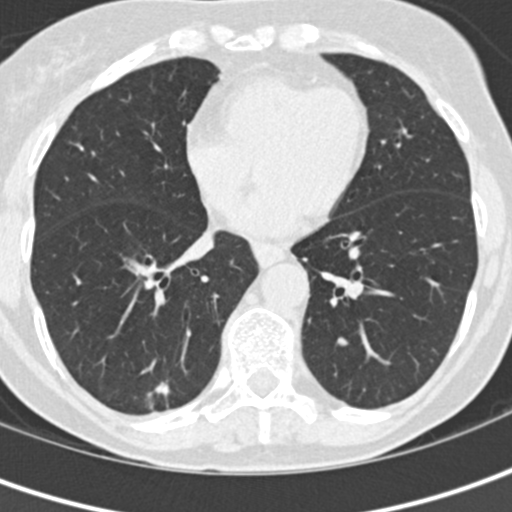
Low-dose screening chest CT, one axial slice. Slice 59 of 152 in the series (ordered by position). Lung window (W 1500 / L -600 HU). 2 mm slice thickness. 512 × 512 image matrix, field of view 280 × 280 mm.
Annotated regions visible in this slice (manually delineated by an expert):
- lesion 1 (tumor, lower lobe of right lung): bounding box [x1, y1, x2, y2] px = [153, 382, 170, 397]